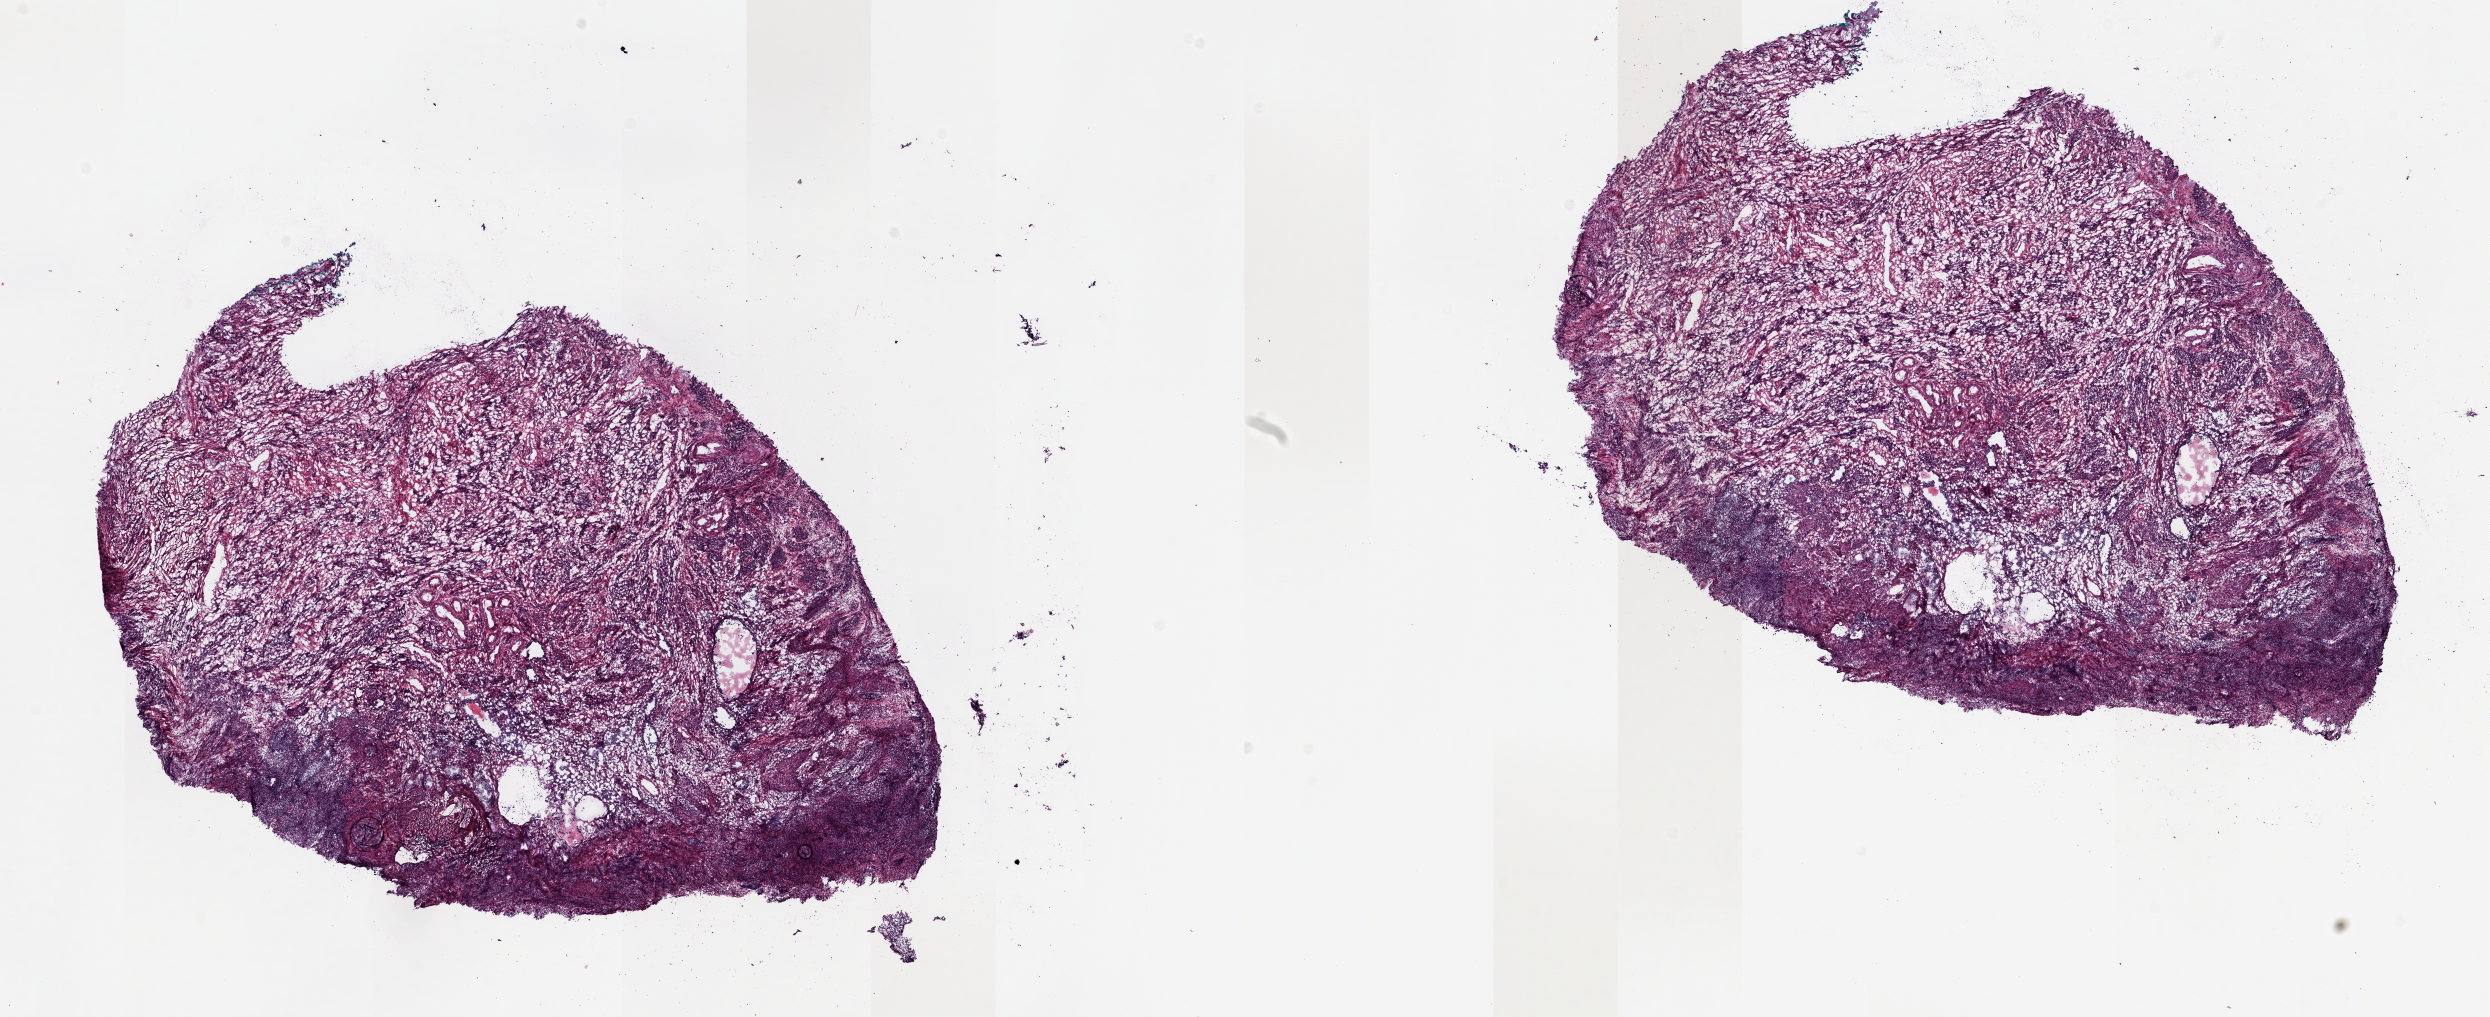
Whole-slide histology image, H&E — a low-resolution overview of the entire scanned area, about 19.8 x 8.1 mm, frozen section from the top of the tissue portion, solid tissue normal (non-tumour tissue) sample from the uterus. Slide review estimates, as recorded: tumour cells 0%, normal cells 100%.
This section: solid tissue normal (non-tumour) sample.